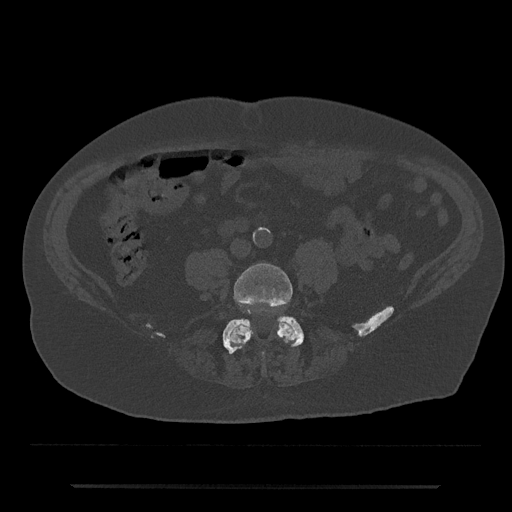
CT including the spine, one axial slice; slice 324 of 797 in the series (ordered by position); bone window (W 1800 / L 400 HU); 512 × 512 image matrix. Patient: male, 80 years. From the clinical record (not read from this slice): primary cancer: prostate.
Annotated regions visible in this slice (semi-automatically segmented with operator editing):
- L4 vertebra: bounding box [x1, y1, x2, y2] px = [228, 263, 297, 356]
- L5 vertebra: [222, 317, 304, 354]